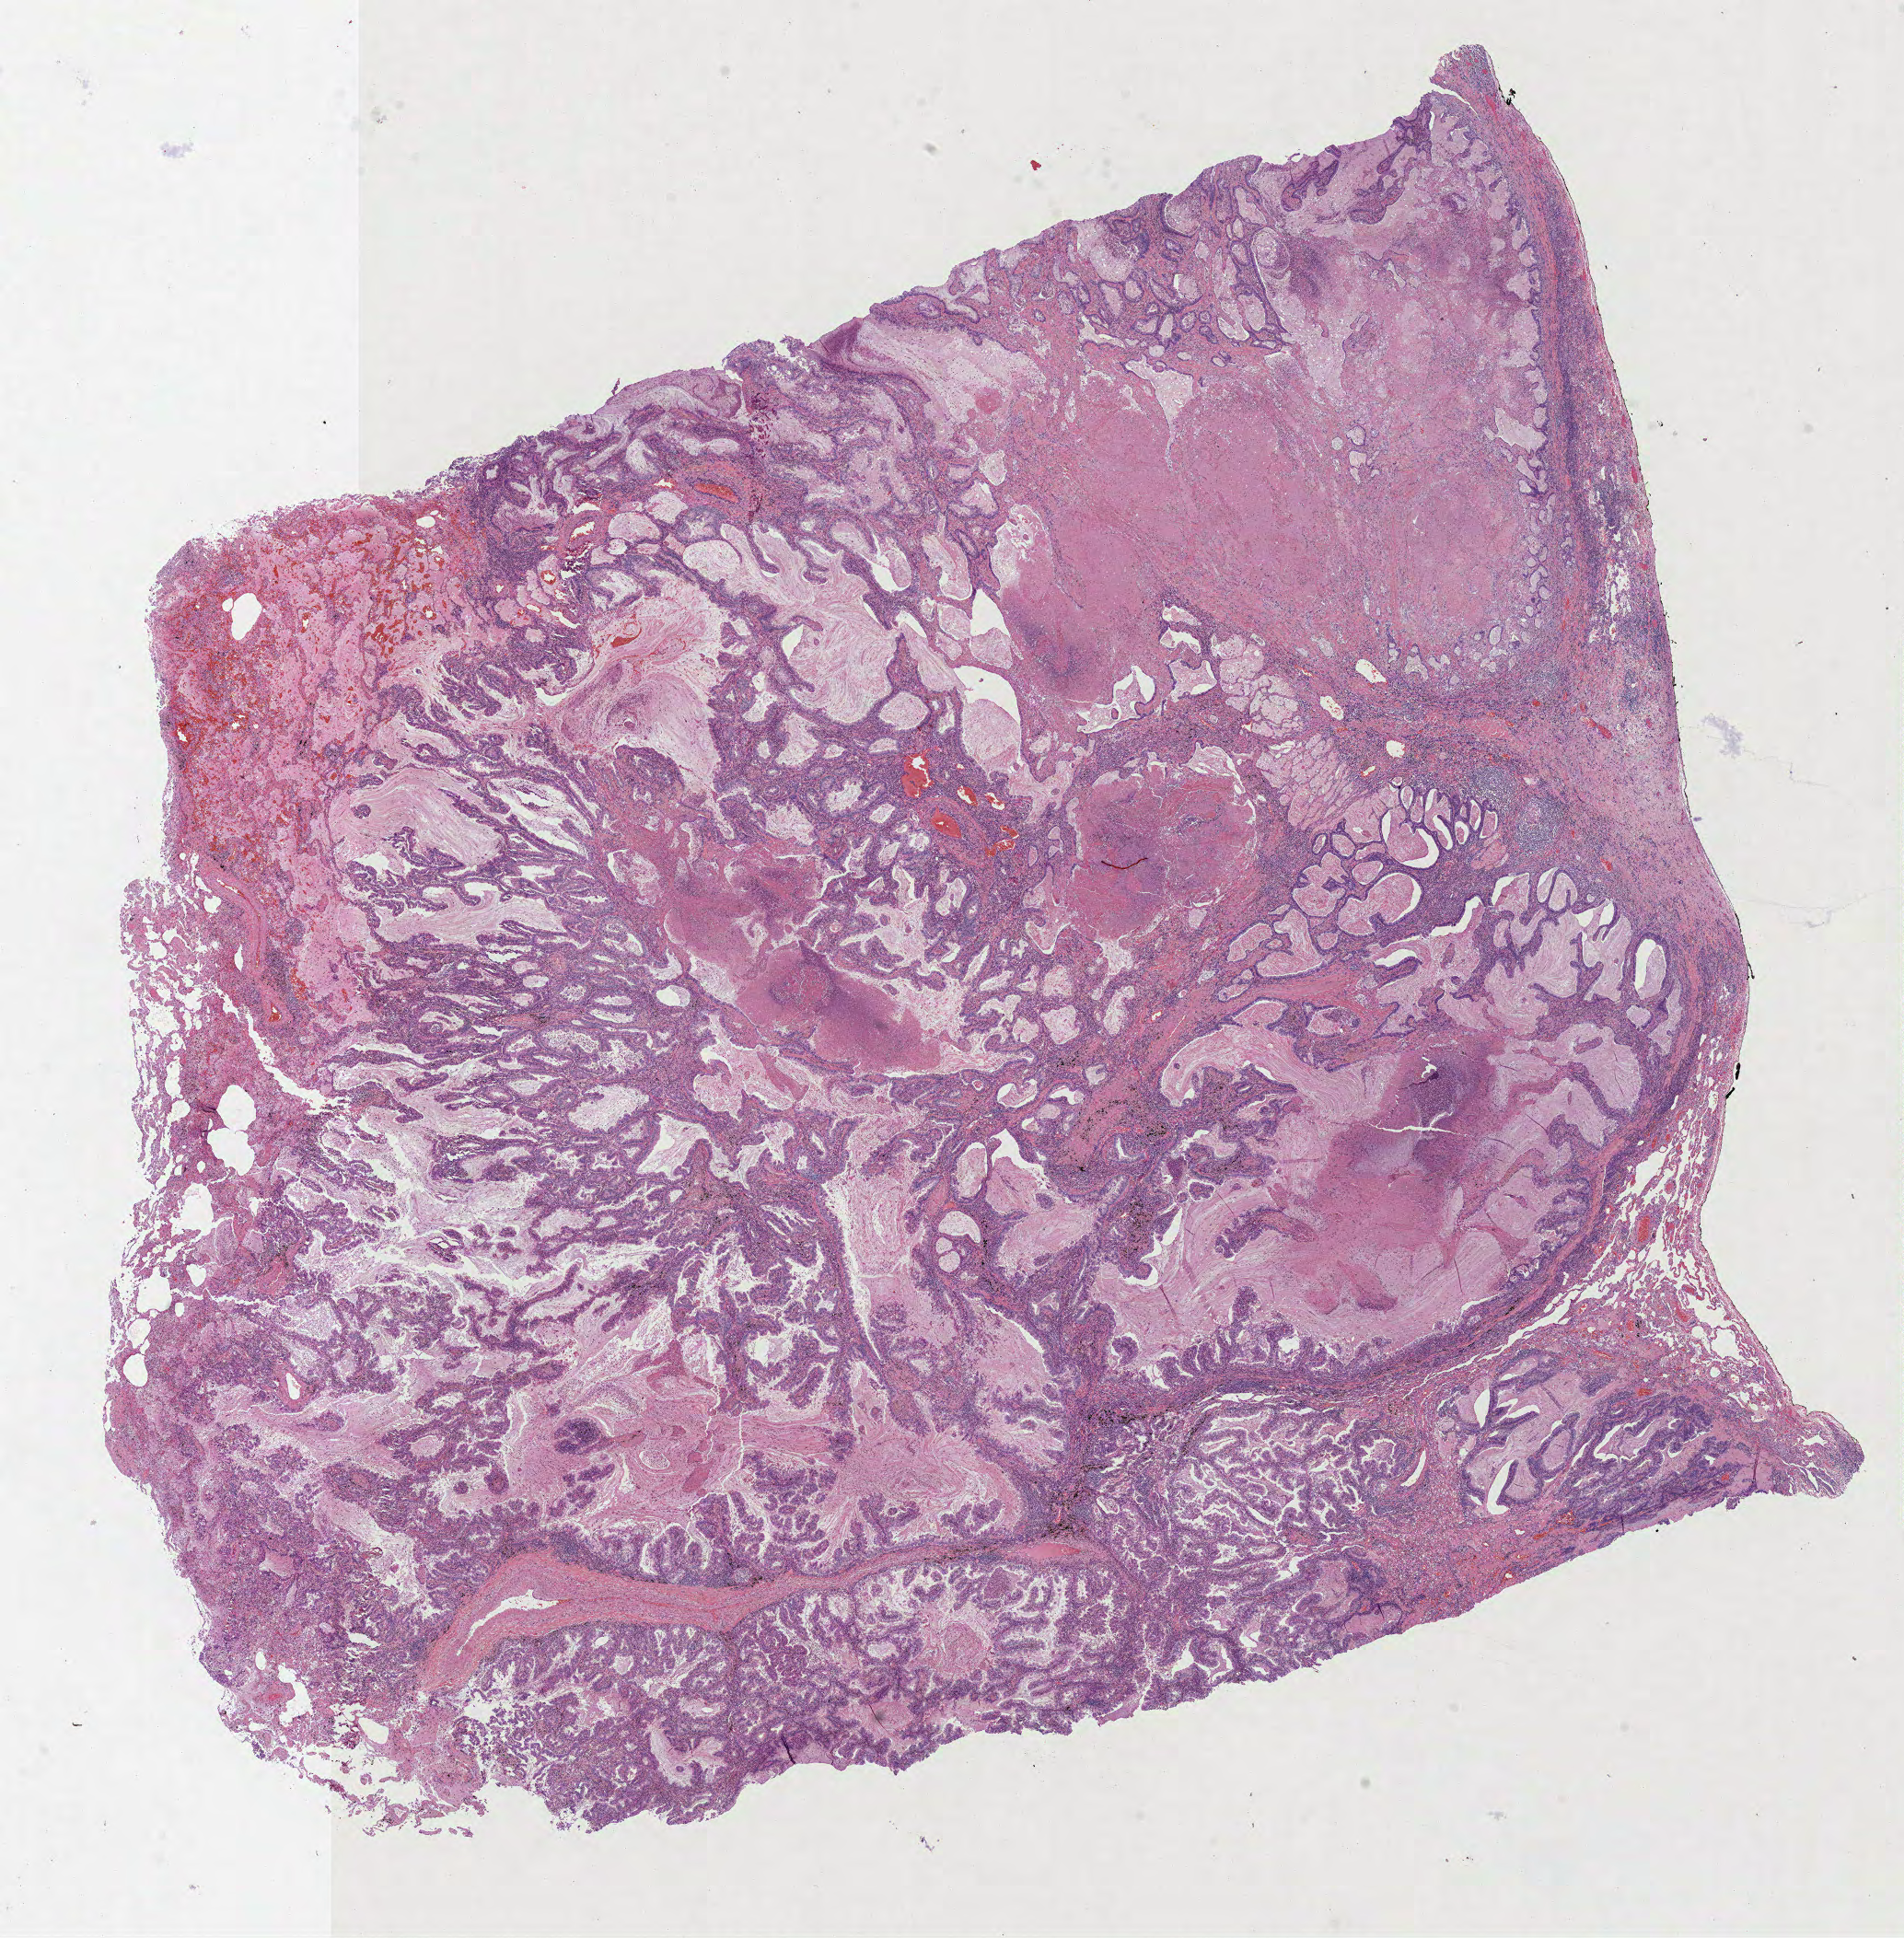
Whole-slide histology image, H&E, shown as a low-resolution overview of the whole scanned area (about 16.7 x 17.0 mm, acquisition: 40x scan), FFPE section, primary tumour sample from the lung. Female, age 60 years at initial diagnosis.
Pathologic diagnosis: Mucinous adenocarcinoma (upper lobe, lung).